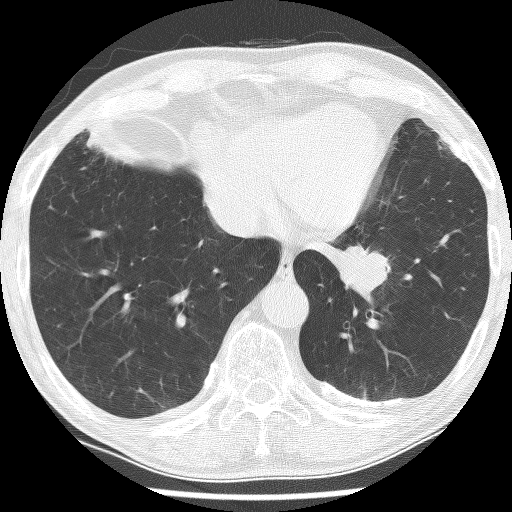
Low-dose screening chest CT, one axial slice; slice 47 of 226 in the series (ordered by position); 120 kVp; lung window (W 1500 / L -600 HU); 2.5 mm slice thickness; 512 × 512 image matrix, field of view 320 × 320 mm.
Annotated regions visible in this slice (expert manual segmentation):
- lesion 1 (tumor, lower lobe of left lung): bounding box [x1, y1, x2, y2] px = [338, 245, 391, 298]